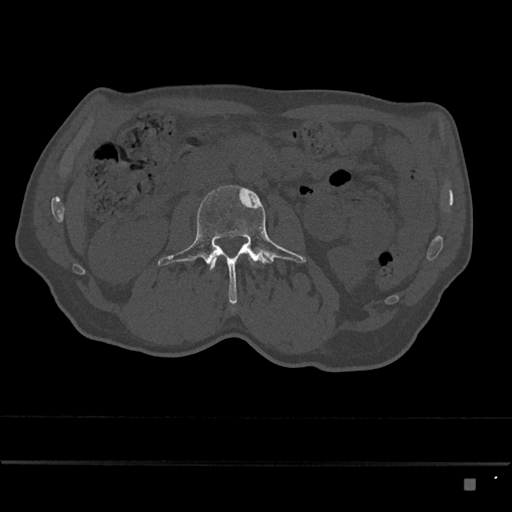
CT including the spine, one axial slice. Slice 417 of 797 in the series (ordered by position). Reconstruction kernel Br40s/3. 120 kVp. Bone window (W 1800 / L 400 HU). 0.5 mm slice thickness. 512 × 512 image matrix. Patient: male, 72 years. From the clinical record (not read from this slice): primary cancer: prostate.
Structures marked on this image (semi-automatic segmentation, software-assisted and operator-edited):
- L2 vertebra: bounding box (x1, y1, x2, y2) in pixels: (210, 255, 253, 271)
- L3 vertebra: (158, 185, 306, 305)